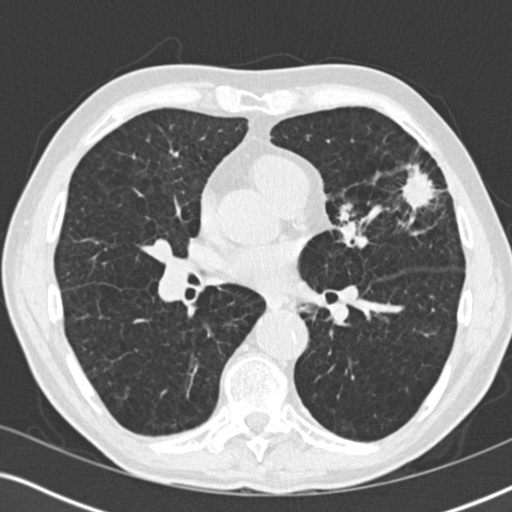
Low-dose screening chest CT, one axial slice; slice 96 of 196 in the series (ordered by position); reconstruction kernel B30f; 120 kVp; lung window (W 1500 / L -600 HU); 2 mm slice thickness; 512 × 512 image matrix.
Outlined on this slice (manually delineated by an expert):
- lesion 1 (tumor, upper lobe of left lung): bounding box [x1, y1, x2, y2] px = [401, 166, 436, 212]
- lesion 2 (tumor, upper lobe of left lung): [339, 210, 351, 222]